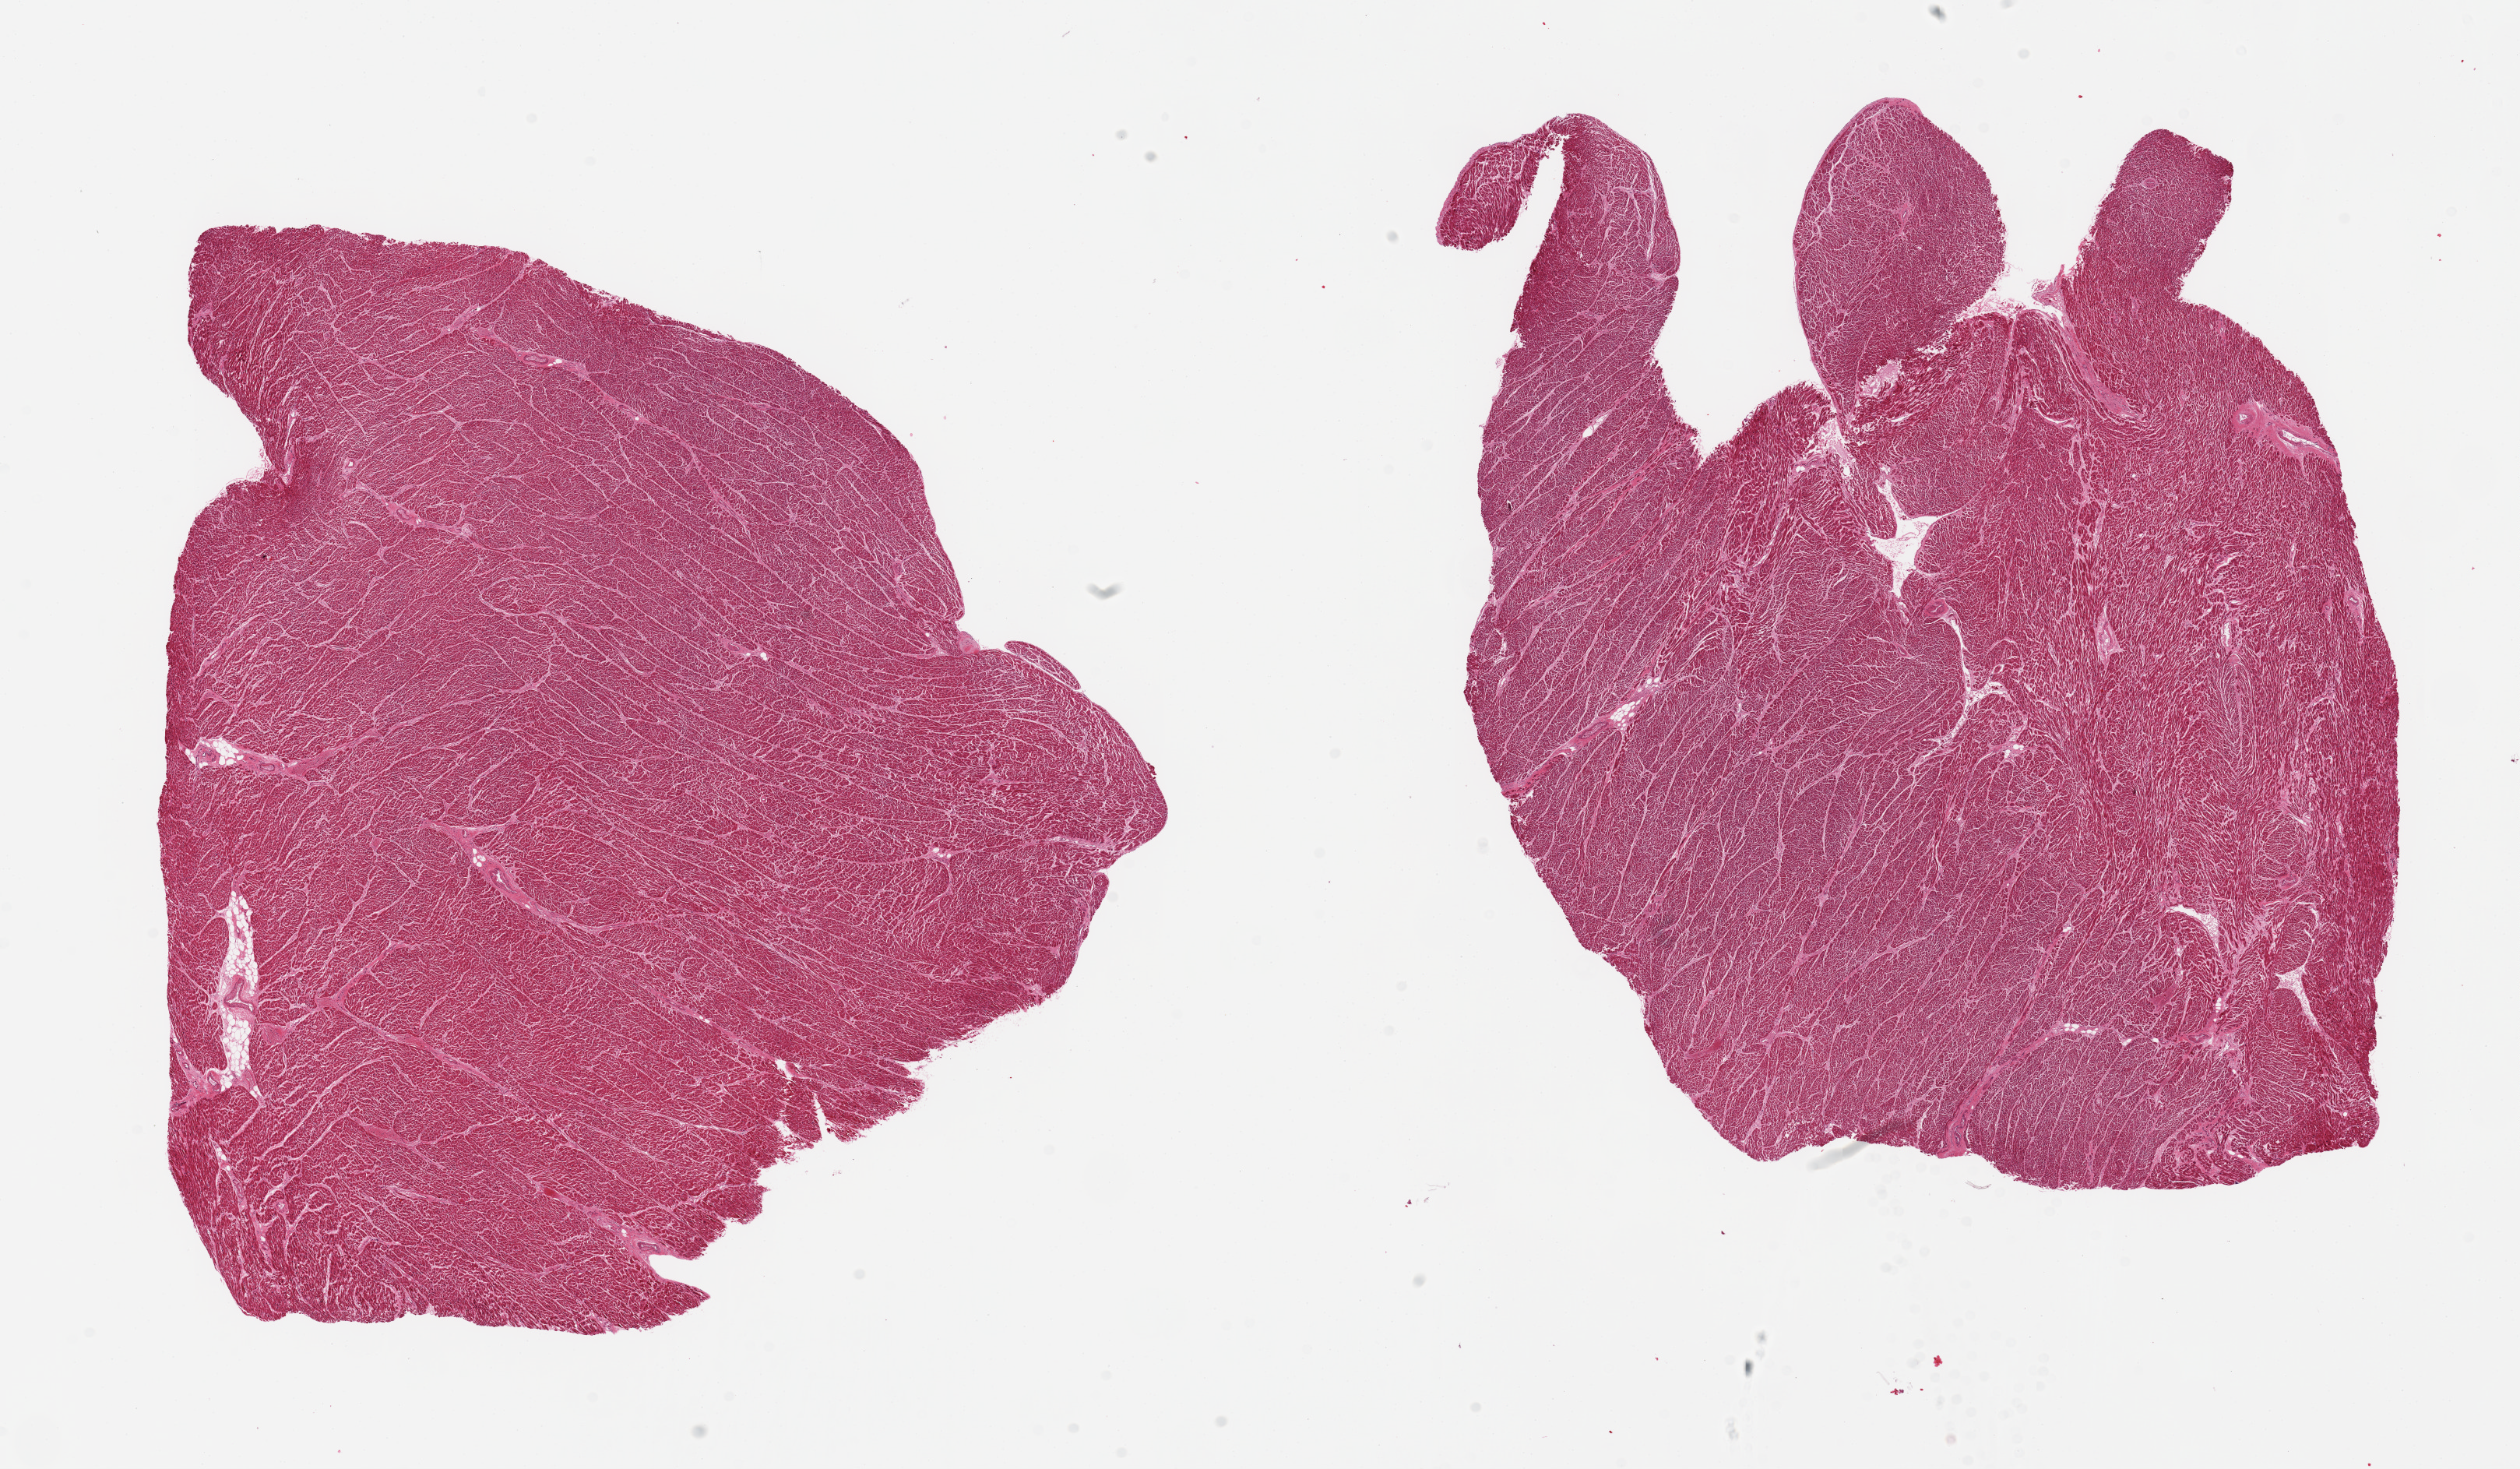
Whole-slide image, hematoxylin and eosin (H&E) stain, a low-resolution overview of the entire scanned area, about 25.6 x 14.9 mm (acquisition: 20x scan). PAXgene-fixed paraffin-embedded (PFPE) section. Section of heart (target tissue). Tissue donor sample. Donor: male.
Pathologist's review note for this sample: 2 pieces; hypertrophied myofibers.